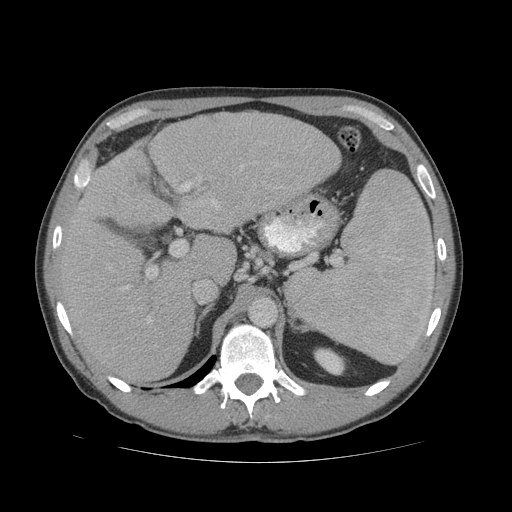
Contrast-enhanced abdominal CT (liver protocol), one axial slice; slice 41 of 81 in the series (ordered by position); reconstruction kernel STANDARD; soft-tissue window (W 400 / L 40 HU); 2.5 mm slice thickness; 512 × 512 image matrix, field of view 400 × 400 mm. From the clinical record (not read from this slice): diagnosis: hepatocellular carcinoma (patient treated with transarterial chemoembolisation; whether this scan precedes or follows treatment is not stated here); TNM stage (as recorded): Stage-IVB; Child-Pugh class: B; tumour differentiation: well differentiated.
Annotated regions visible in this slice (semi-automatic segmentation, software-assisted and operator-edited):
- liver parenchyma outside the tumour (the mass and vessels are separate outlines, so this box may not span the whole liver): bounding box [x1, y1, x2, y2] px = [56, 112, 340, 384]
- liver vessels: [71, 161, 243, 332]